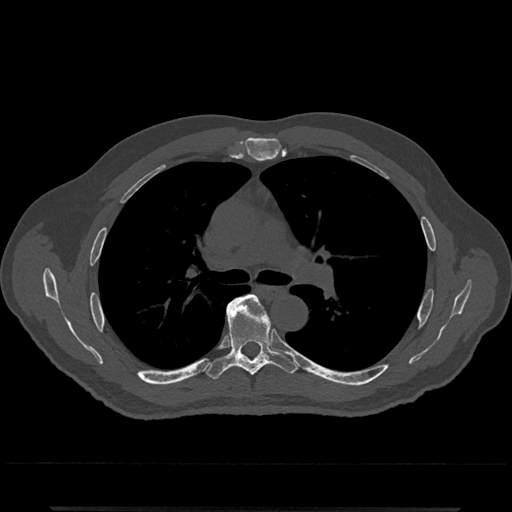
CT including the spine, one axial slice. Slice 783 of 797 in the series (ordered by position). 120 kVp. Bone window (W 1800 / L 400 HU). 0.5 mm slice thickness. 512 × 512 image matrix, field of view 393 × 393 mm. Male patient, age 67 years. Case-level facts recorded for this patient, not image findings: primary cancer: prostate.
Structures marked on this image (semi-automatically segmented with operator editing):
- T5 vertebra: bounding box <238,295,267,314> (left, top, right, bottom; pixels)
- T6 vertebra: <206,295,298,379>